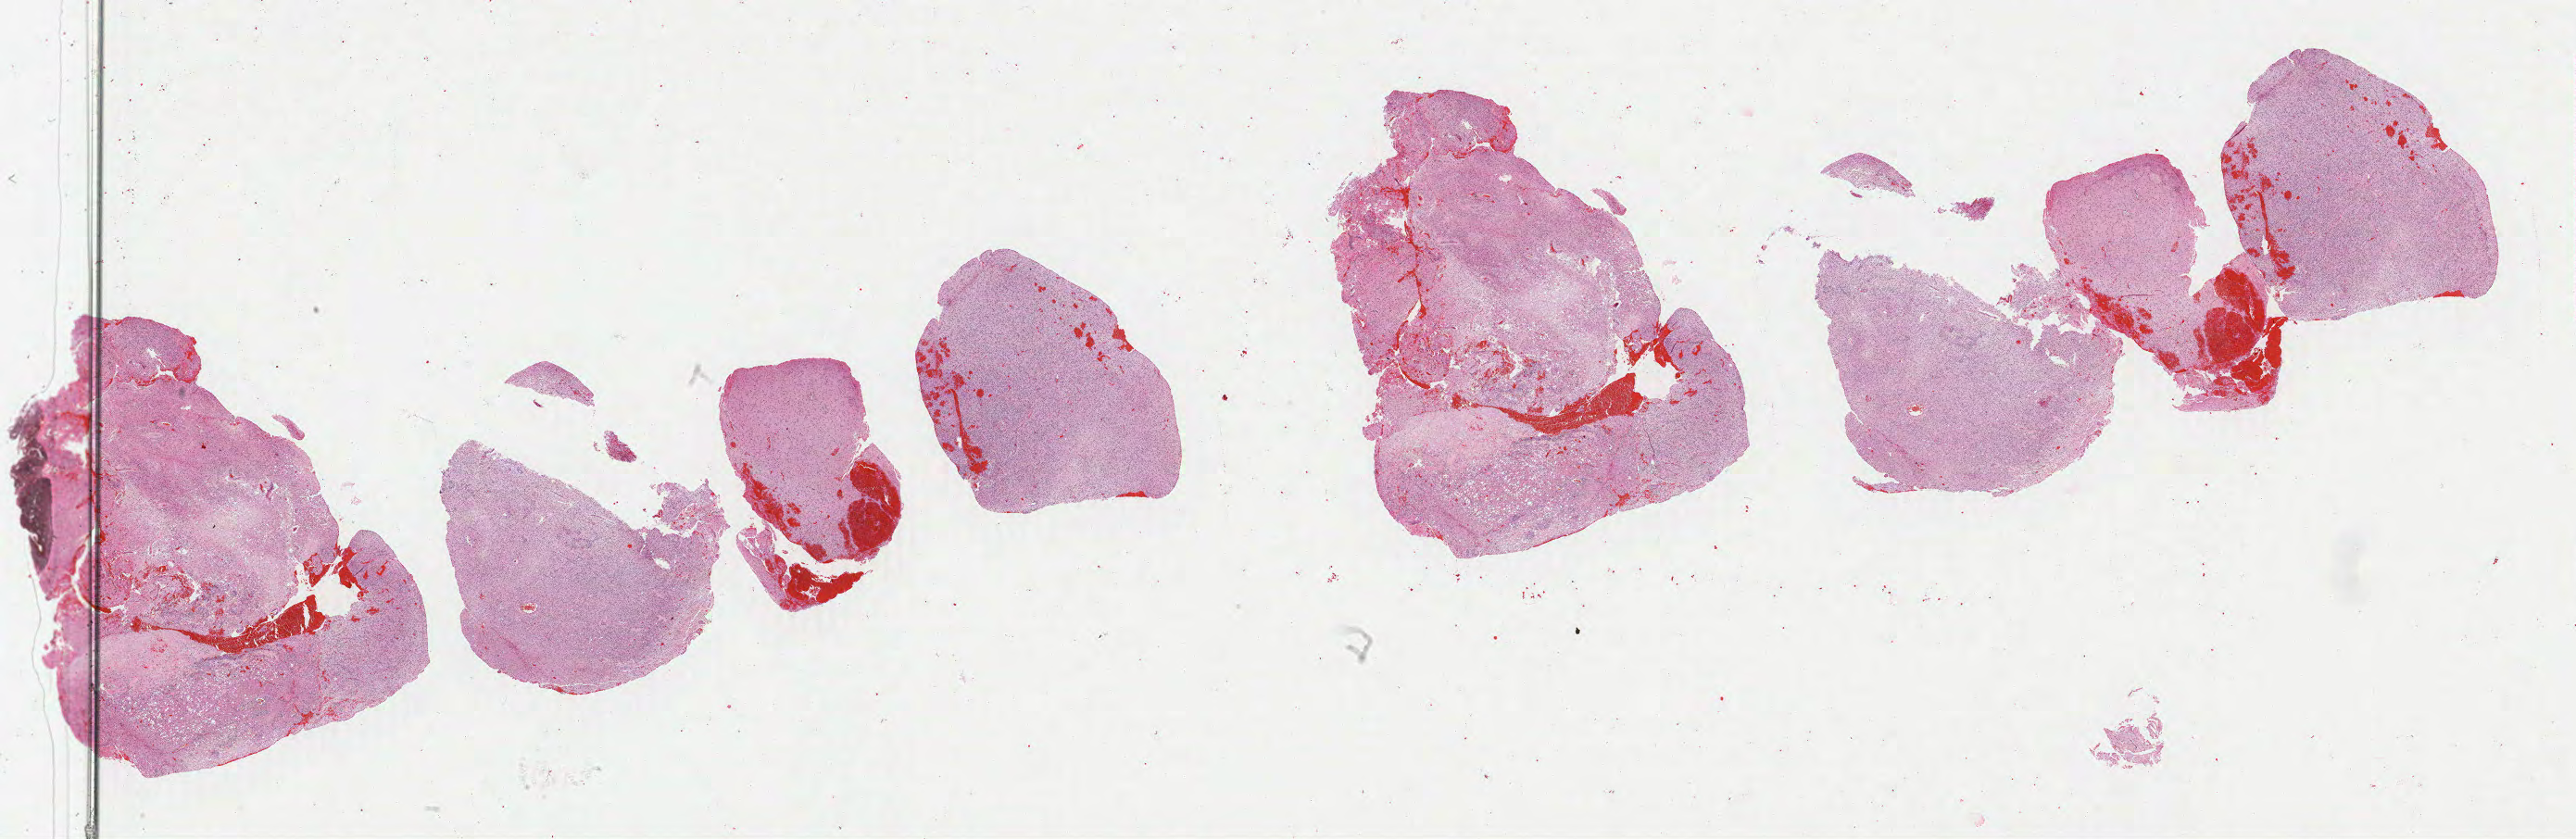
Digitized H&E tissue section (whole slide), shown as a low-resolution overview of the whole scanned area (about 44.3 x 14.4 mm), FFPE section, brain, primary tumour sample. Male, age 48 years at initial diagnosis. Histologic grade: G3 (poorly differentiated).
* laterality: right
* histologic diagnosis: Astrocytoma, anaplastic